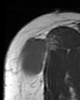
MRI of an extremity soft-tissue mass, one axial slice. Slice 30 of 46 in the series (ordered by position). MR volume resampled by the dataset authors to the PET/CT grid (not the native acquisition matrix). 3.27 mm slice thickness. 80 × 100 image matrix, field of view 78 × 98 mm. Female patient. Case-level facts recorded for this patient, not image findings: histological type: synovial sarcoma; grade: intermediate; site of the primary tumour: right thigh.
Structures marked on this image (expert contour drawn on MRI and transferred to this co-registered scan by the dataset authors):
- gross tumour volume including surrounding oedema: bounding box <18,35,54,79> (left, top, right, bottom; pixels)
- gross tumour volume (mass): <18,37,52,79>